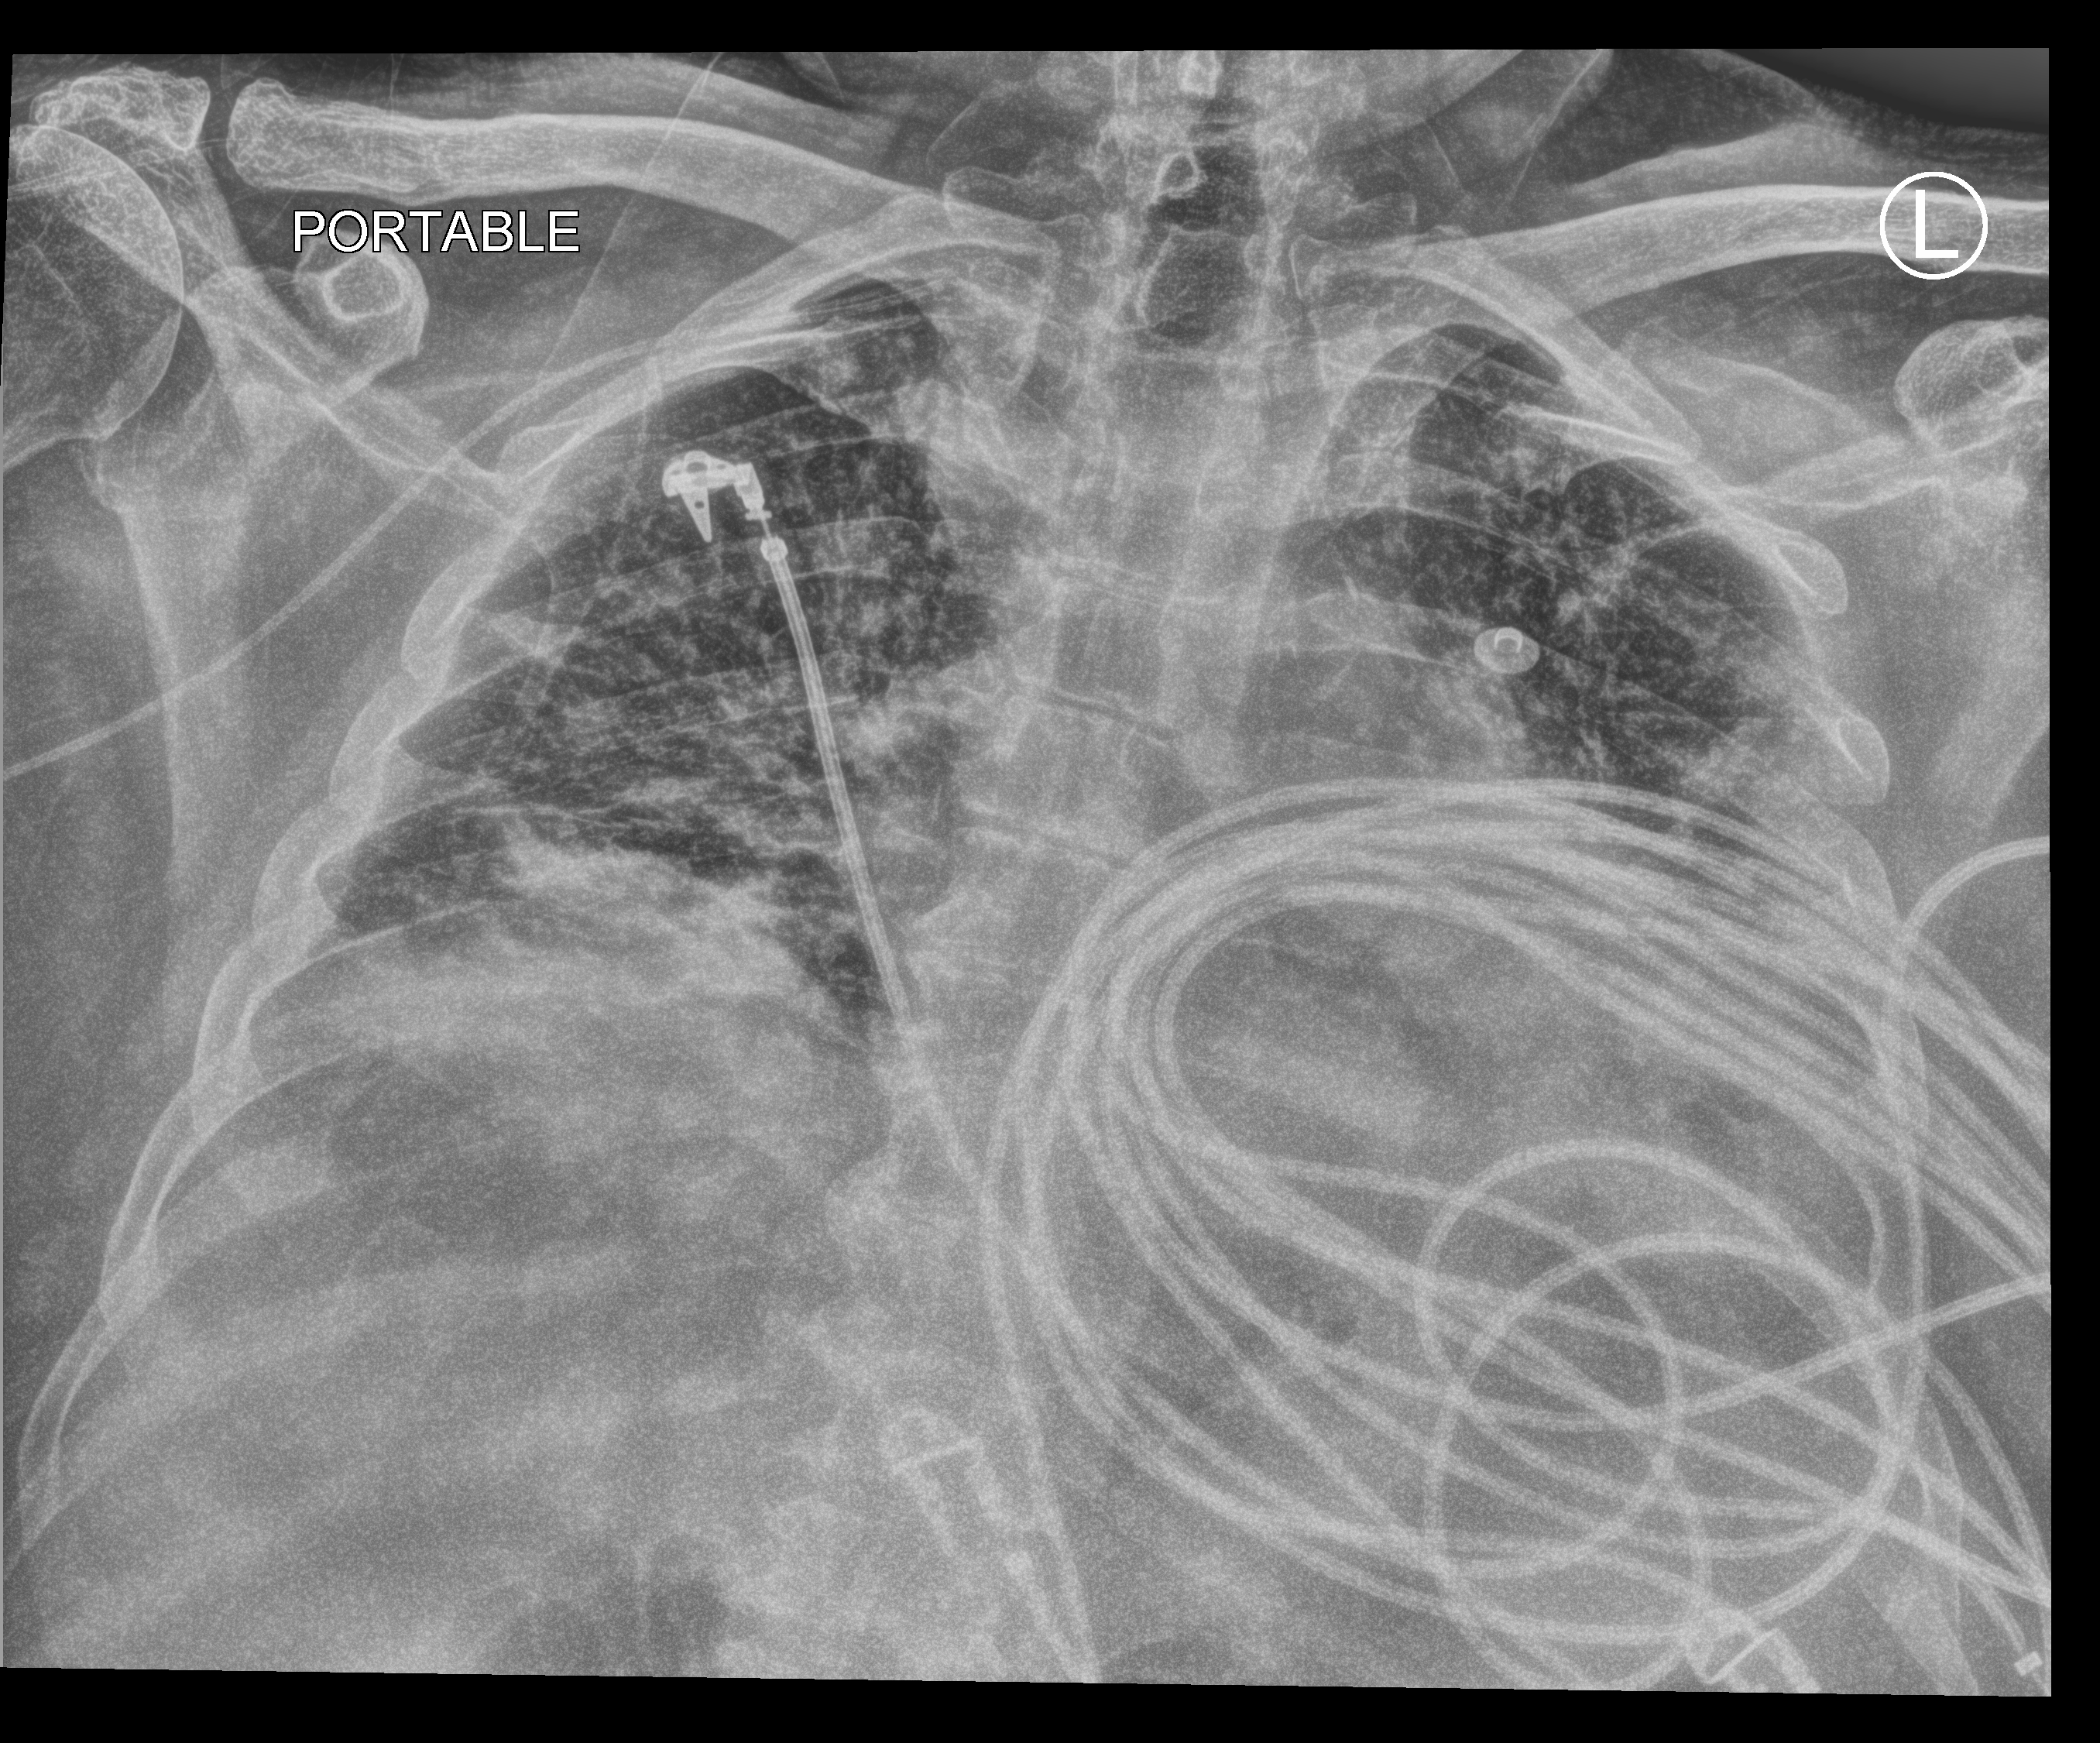
Bedside chest radiograph (computed radiography), anteroposterior (AP) projection. Male patient hospitalised with COVID-19, age 60–74 years.
Admission-level facts for this patient (not findings on this image; timing relative to this image not recorded): other chronic lung disease (admission record): no.